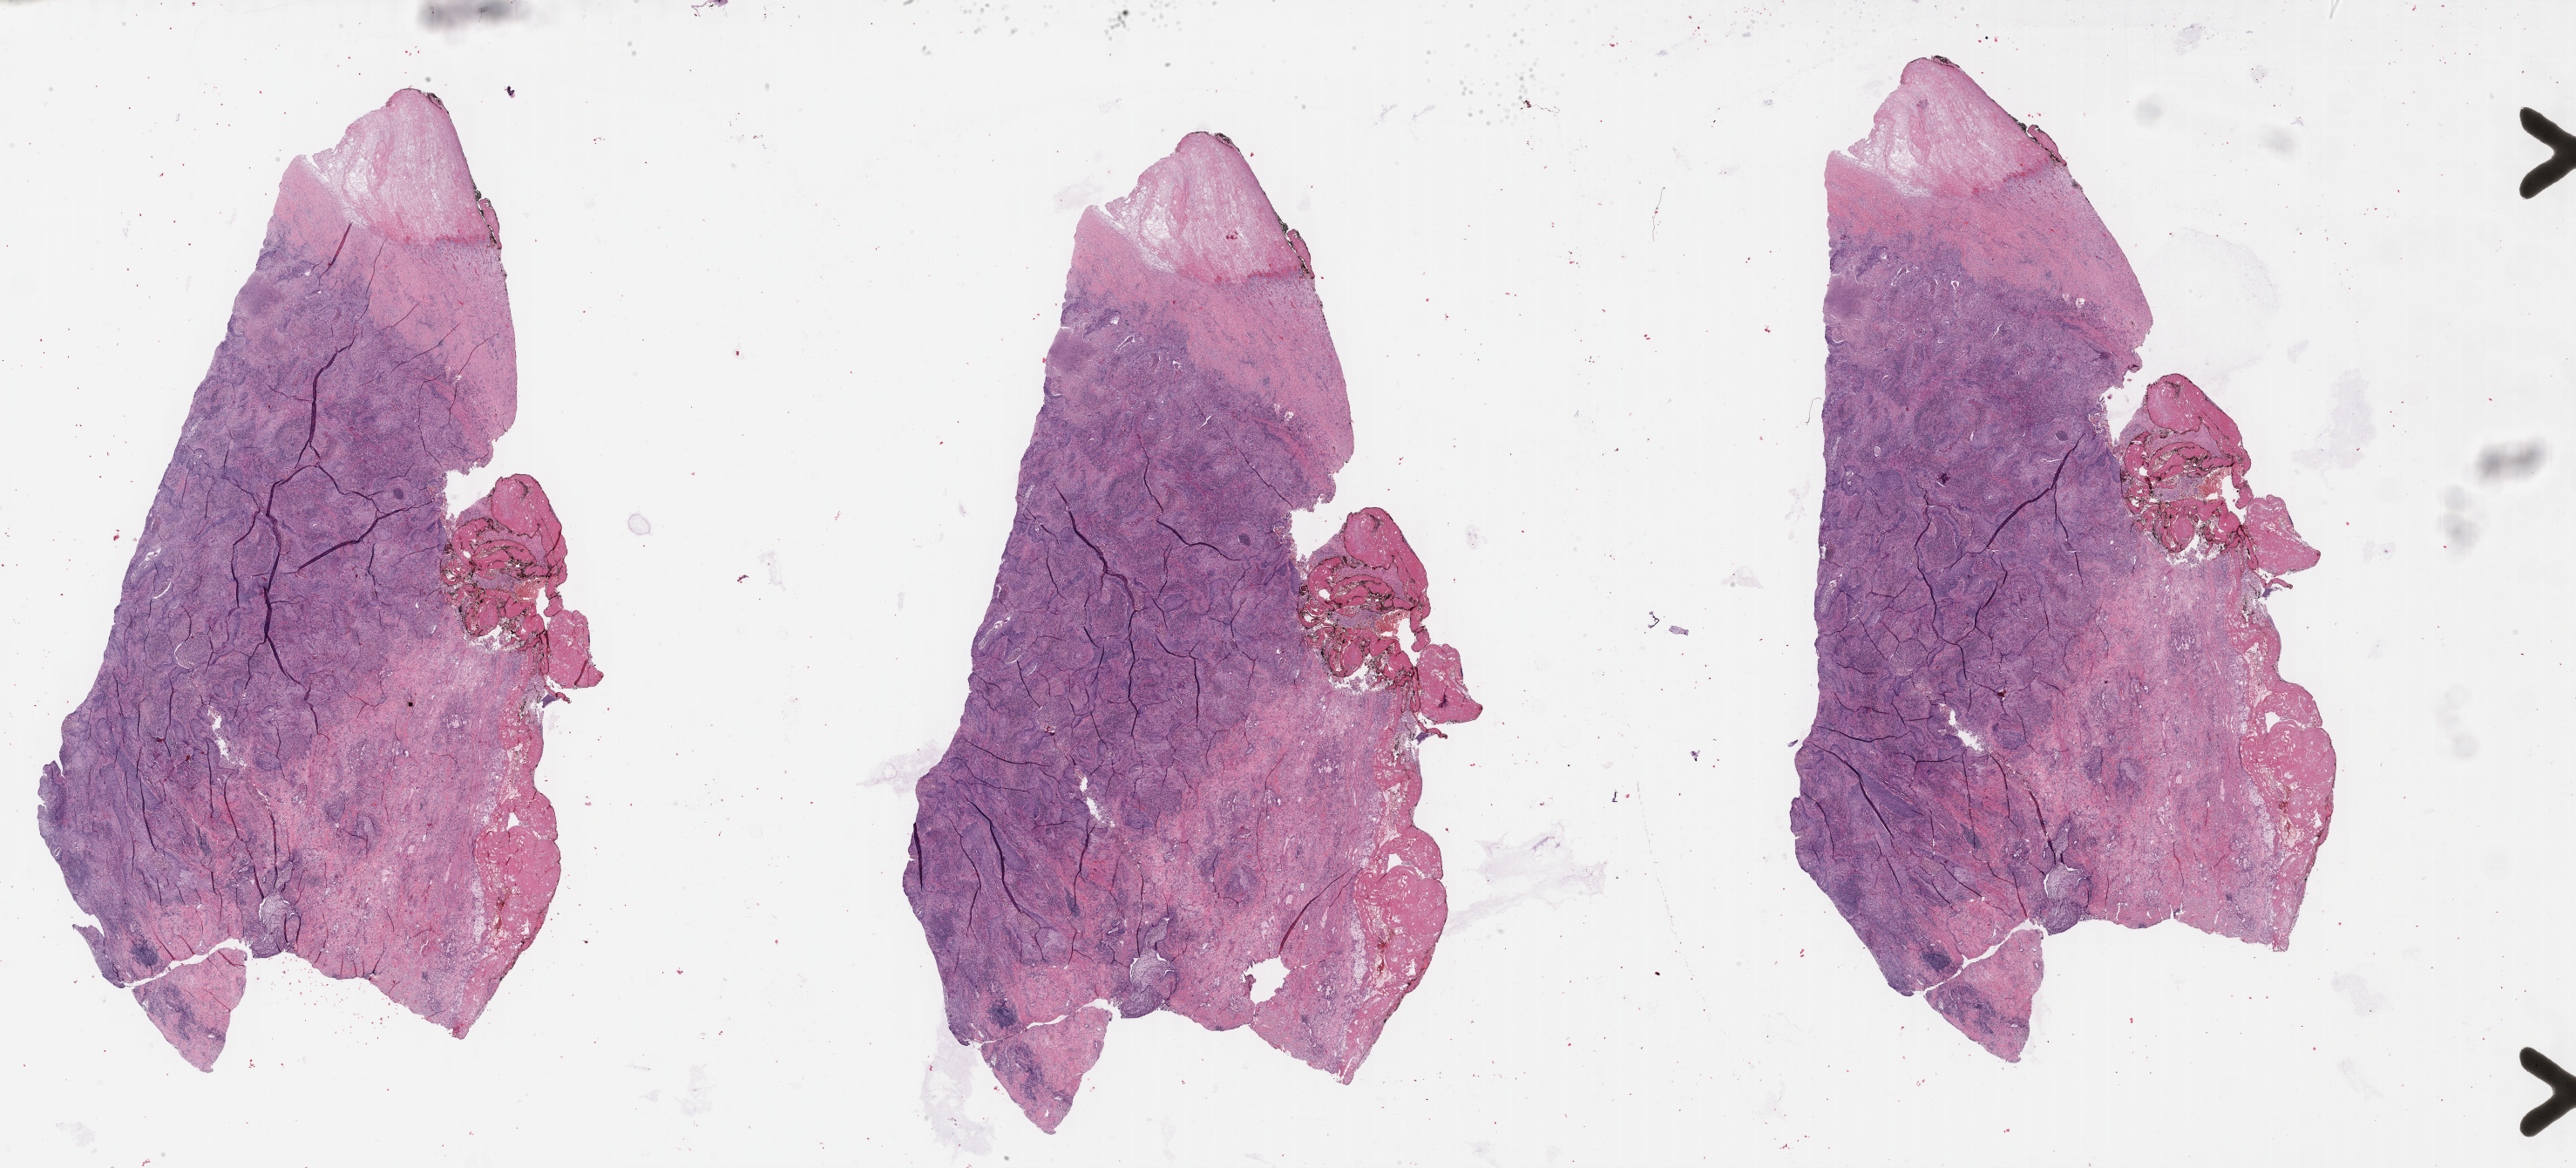
Digitized H&E-stained tissue section (whole slide), a low-resolution overview of the entire scanned area, about 47.8 x 21.7 mm. Formalin-fixed paraffin-embedded (FFPE) diagnostic section. Sample: primary tumour, lung. Male, age 73 years at initial diagnosis.
AJCC pathologic stage: IIA. Pathologic diagnosis: Squamous cell carcinoma, NOS (lower lobe, lung).